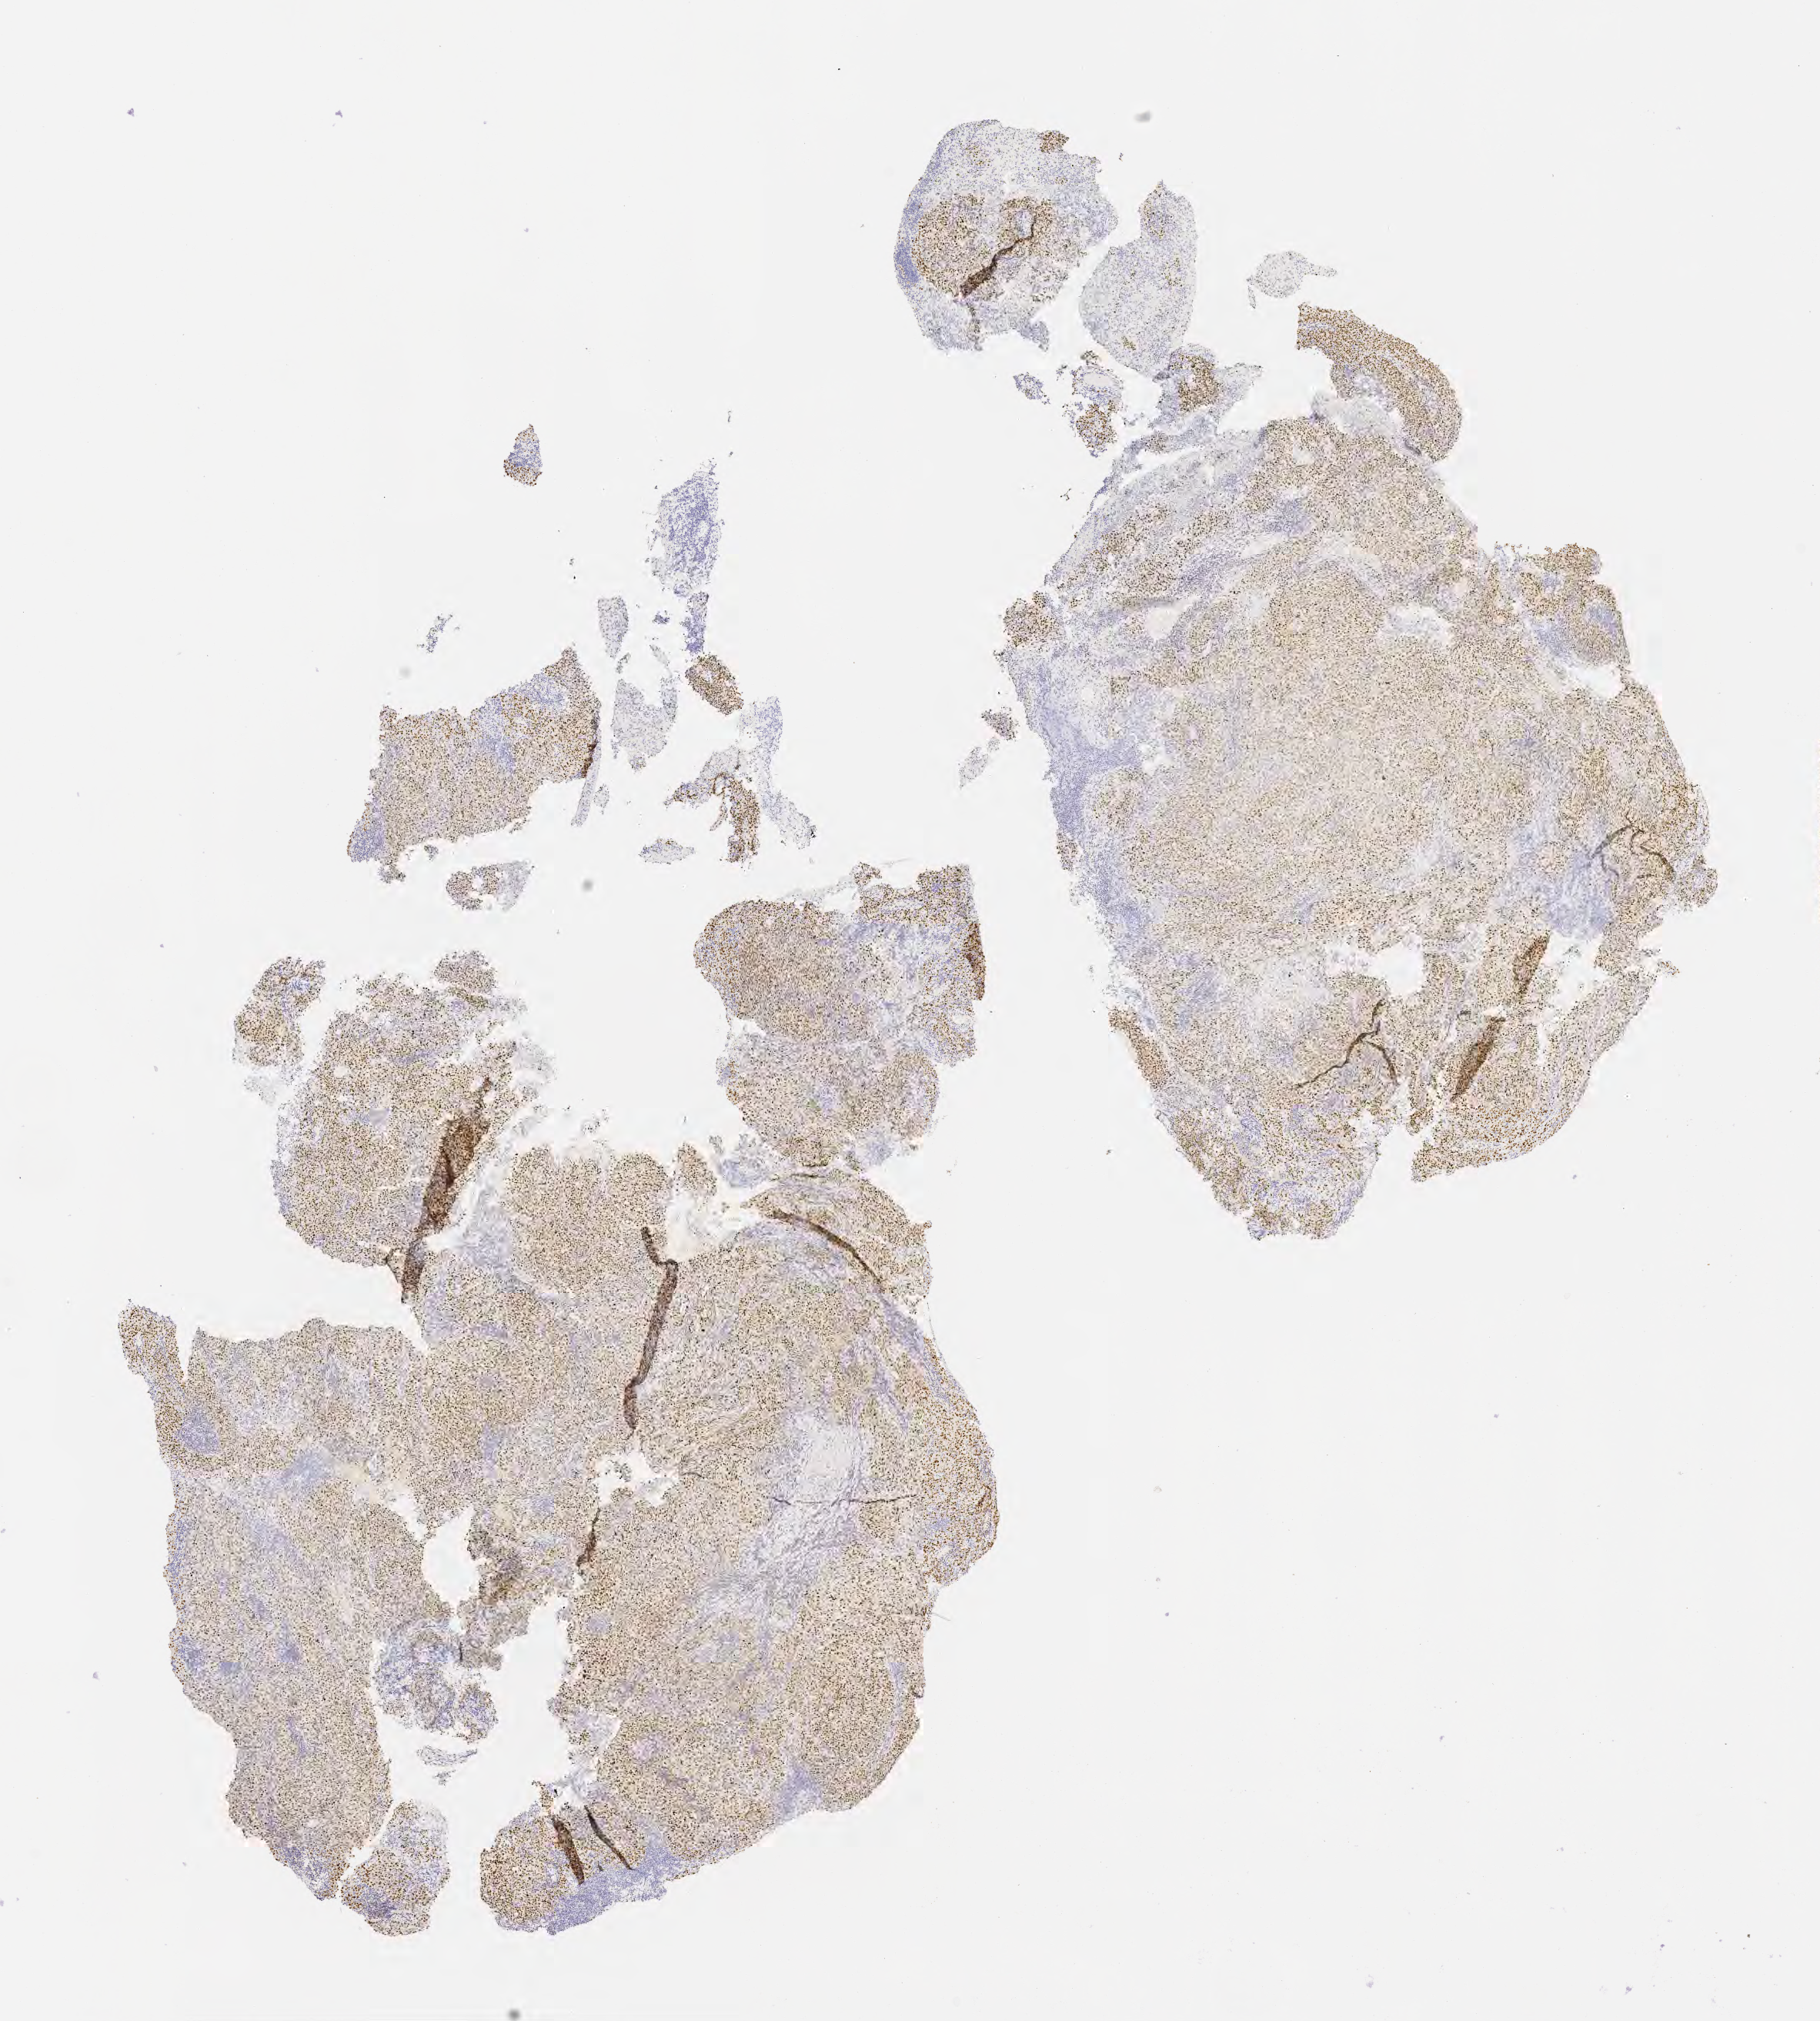
IHC for p53, whole-slide image — a low-resolution overview of the entire scanned area, about 9.6 x 10.6 mm, tumor tissue, anatomic site: cervix. Patient: female, age 70 years.
Diagnosis: Squamous cell carcinoma, large cell, nonkeratinizing, NOS.